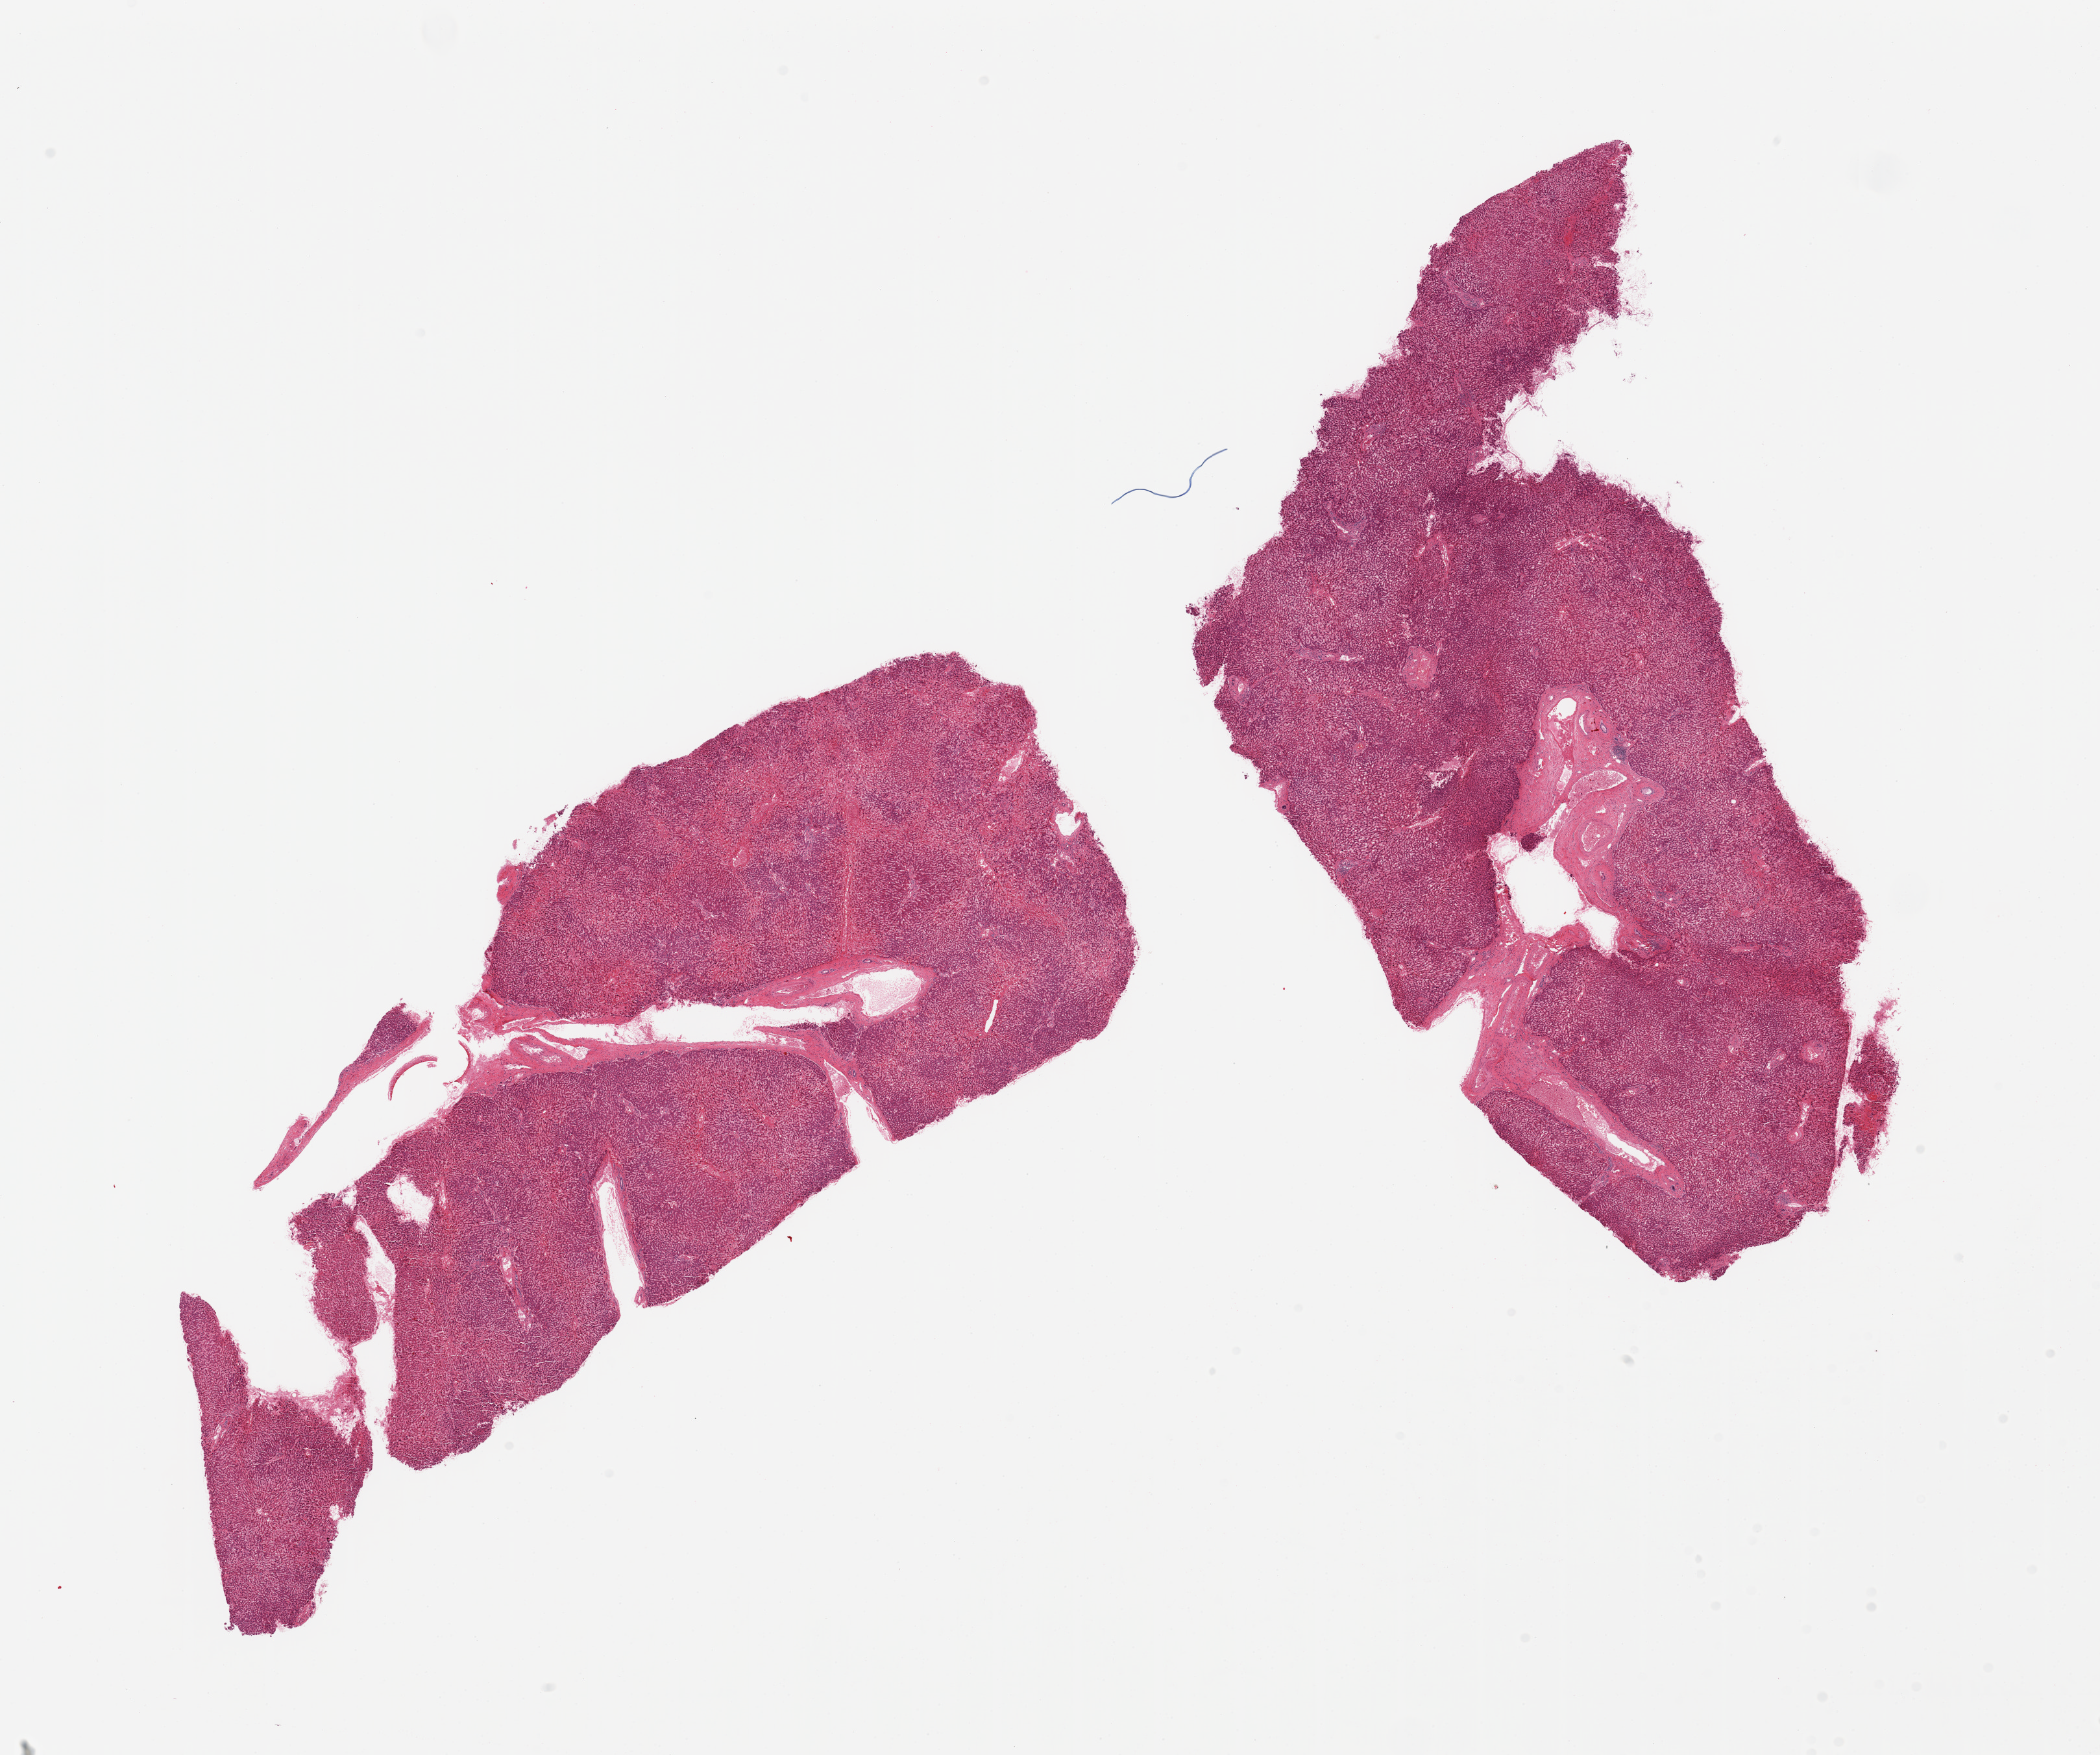
Digitized H&E-stained section, brightfield, shown as a low-resolution overview of the whole scanned area (about 25.6 x 21.4 mm, from a 20x scan), PAXgene-fixed, paraffin-embedded tissue, target tissue: liver, tissue donor sample. Male donor.
Review note (as recorded): 2 pieces, moderte congestion.